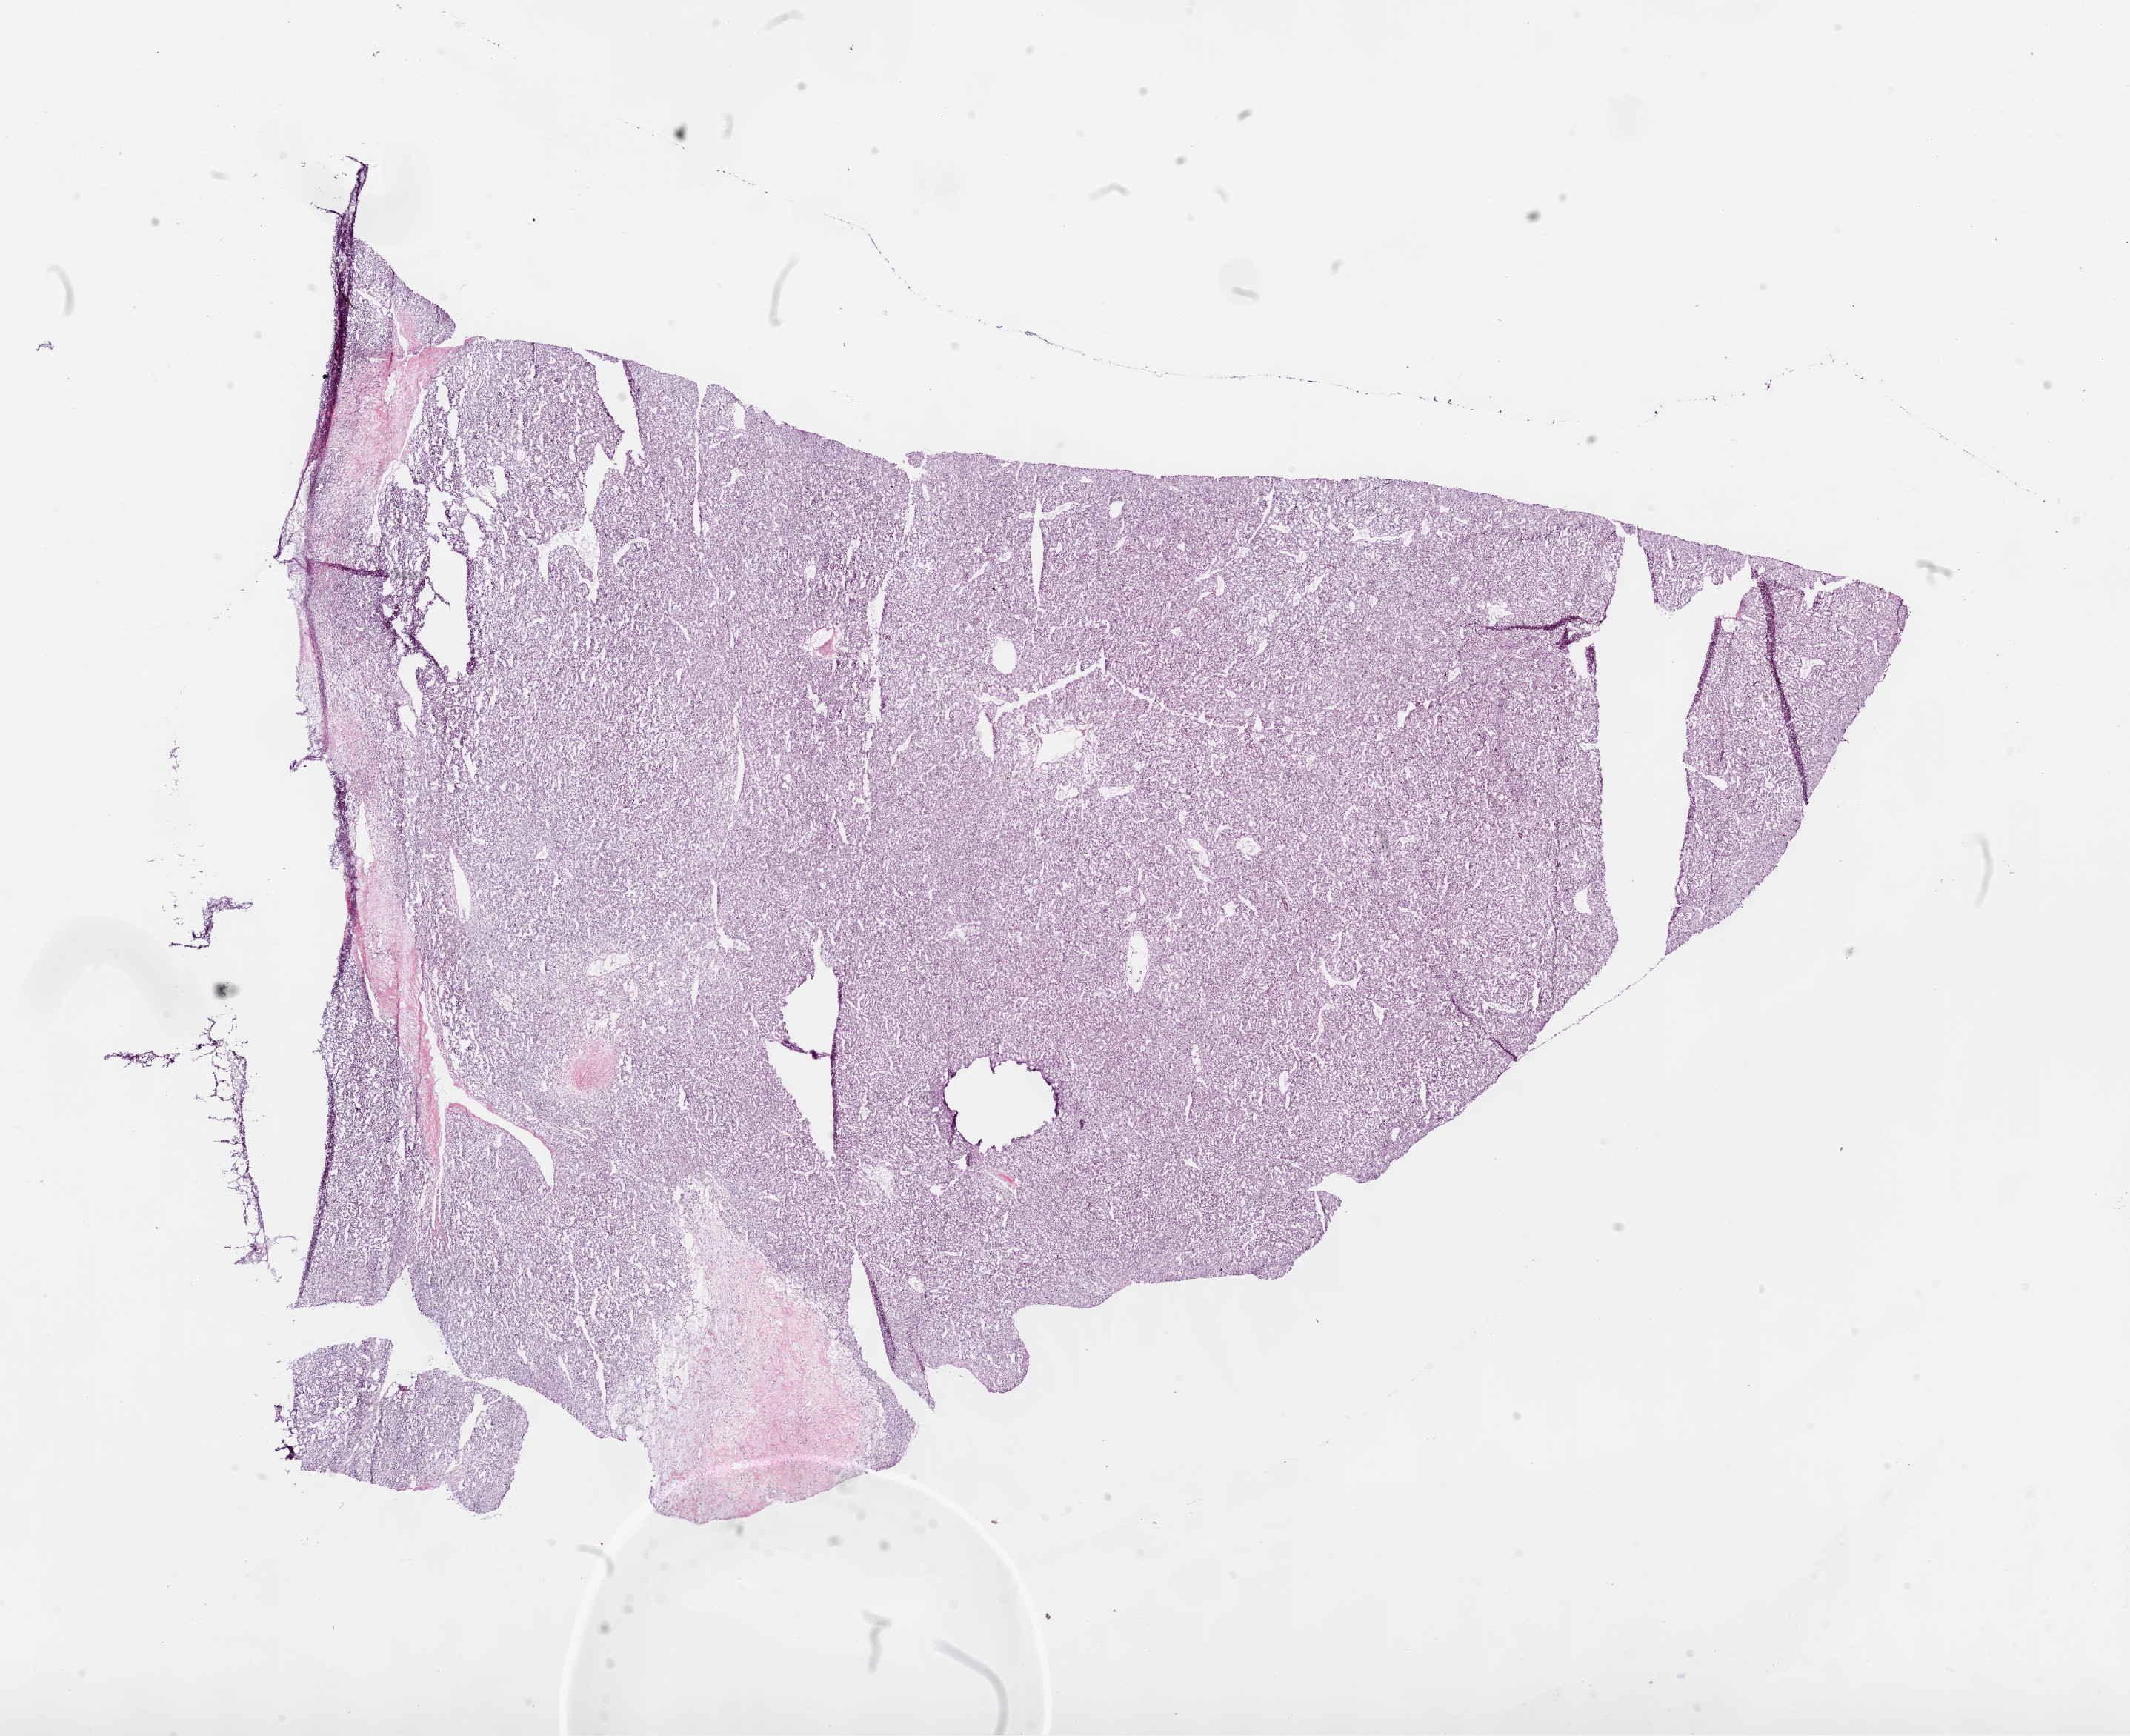
Hematoxylin and eosin (H&E) stained whole-slide image — a low-resolution overview of the entire scanned area, about 23.1 x 18.8 mm, frozen section from the bottom of the tissue portion, primary tumour sample from the kidney. Patient: female, age at initial diagnosis 70 years. Histologic grade: G2 (moderately differentiated). Pathologist review of this section (percent, as recorded): tumour cells 95%, tumour nuclei 85%, normal cells 0%, stromal cells 5%, necrosis 0%.
AJCC pathologic stage: I. Pathologic diagnosis: Clear cell adenocarcinoma, NOS. Laterality: right.